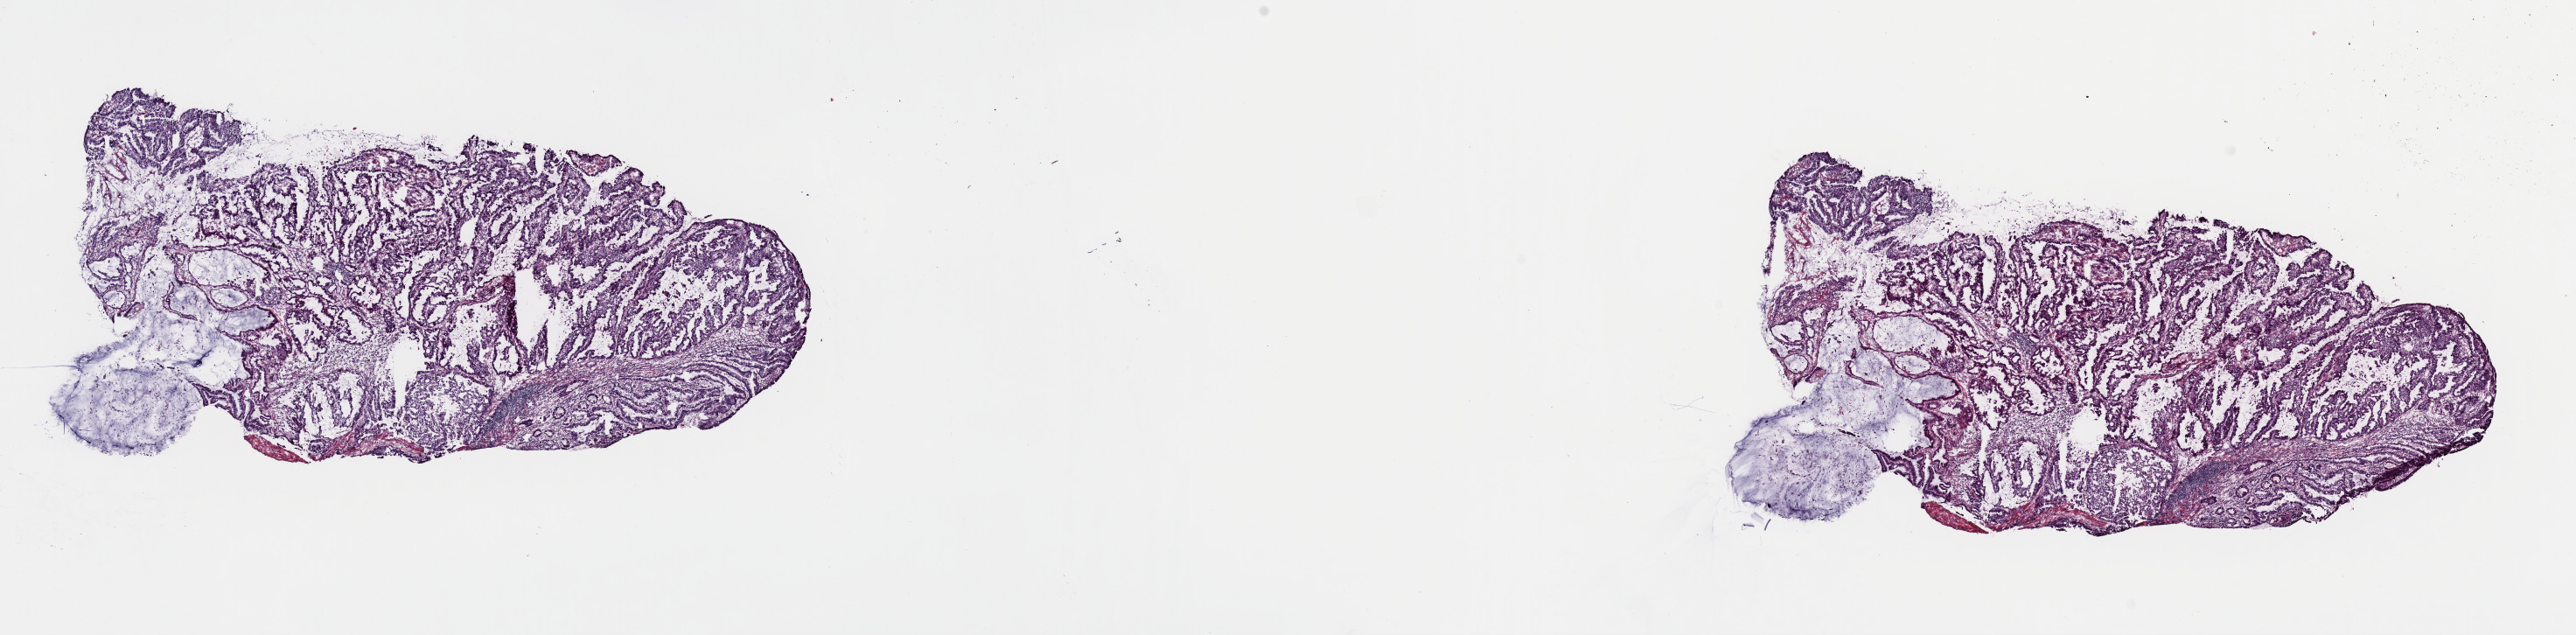
Whole-slide histology image, H&E — low-resolution overview of the scanned area, about 23.3 x 5.7 mm (acquisition: 40x scan); frozen section; stomach, primary tumour sample. Patient: male, age at initial diagnosis 75 years.
Pathologic diagnosis: Tubular adenocarcinoma (body of stomach).